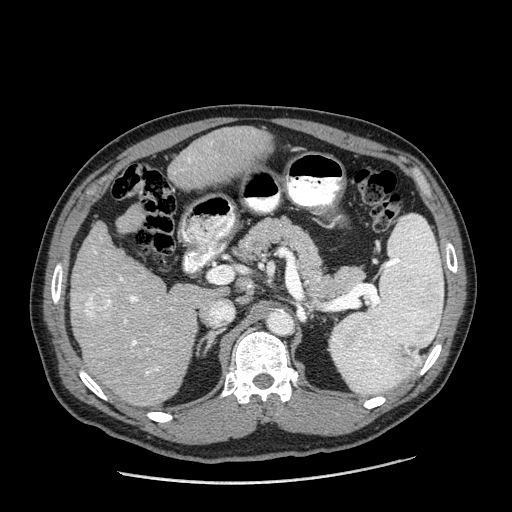
Contrast-enhanced abdominal CT (liver protocol), one axial slice; slice 101 of 198 in the series (ordered by position); 120 kVp; one of 2 acquisitions stored at this slice position; soft-tissue window (W 400 / L 40 HU); 512 × 512 image matrix, field of view 400 × 400 mm. From the clinical record (not read from this slice): diagnosis: hepatocellular carcinoma (patient treated with transarterial chemoembolisation; whether this scan precedes or follows treatment is not stated here); TNM stage (as recorded): Stage-II; Child-Pugh class: A; tumour differentiation: moderately differentiated; tumour nodularity: multinodular.
Structures marked on this image (semi-automatically segmented with operator editing):
- liver parenchyma outside the tumour (the mass and vessels are separate outlines, so this box may not span the whole liver): bounding box (x1, y1, x2, y2) in pixels: (70, 126, 272, 406)
- mass: (79, 286, 119, 324)
- liver vessels: (94, 158, 191, 374)